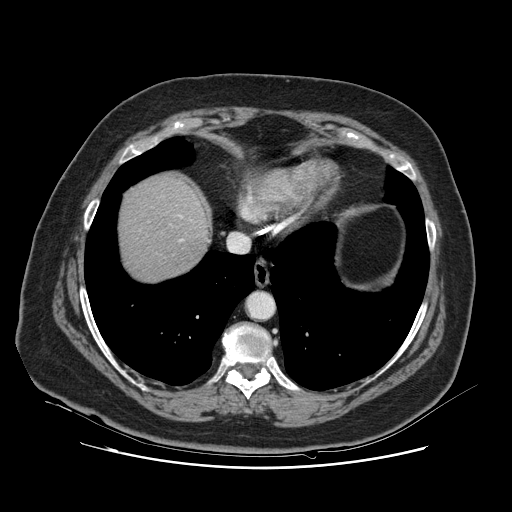
Contrast-enhanced abdominal CT, one axial slice; position 112 of 132 along the scan axis; intravenous contrast given; soft-tissue window (W 400 / L 40 HU); 512 × 512 image matrix, field of view 391 × 391 mm. Female patient, age 73 years. From the clinical record (not read from this slice): diagnosis: colorectal cancer liver metastases, imaged before liver resection; multiple liver metastases: no; largest metastasis: 7 cm; disease in both lobes: no.
Outlined on this slice (expert manual segmentation):
- hepatic veins: bounding box [x1, y1, x2, y2] px = [180, 215, 182, 241]
- liver: [119, 176, 208, 281]
- planned liver remnant (the part of the liver to remain after resection): [119, 175, 208, 281]